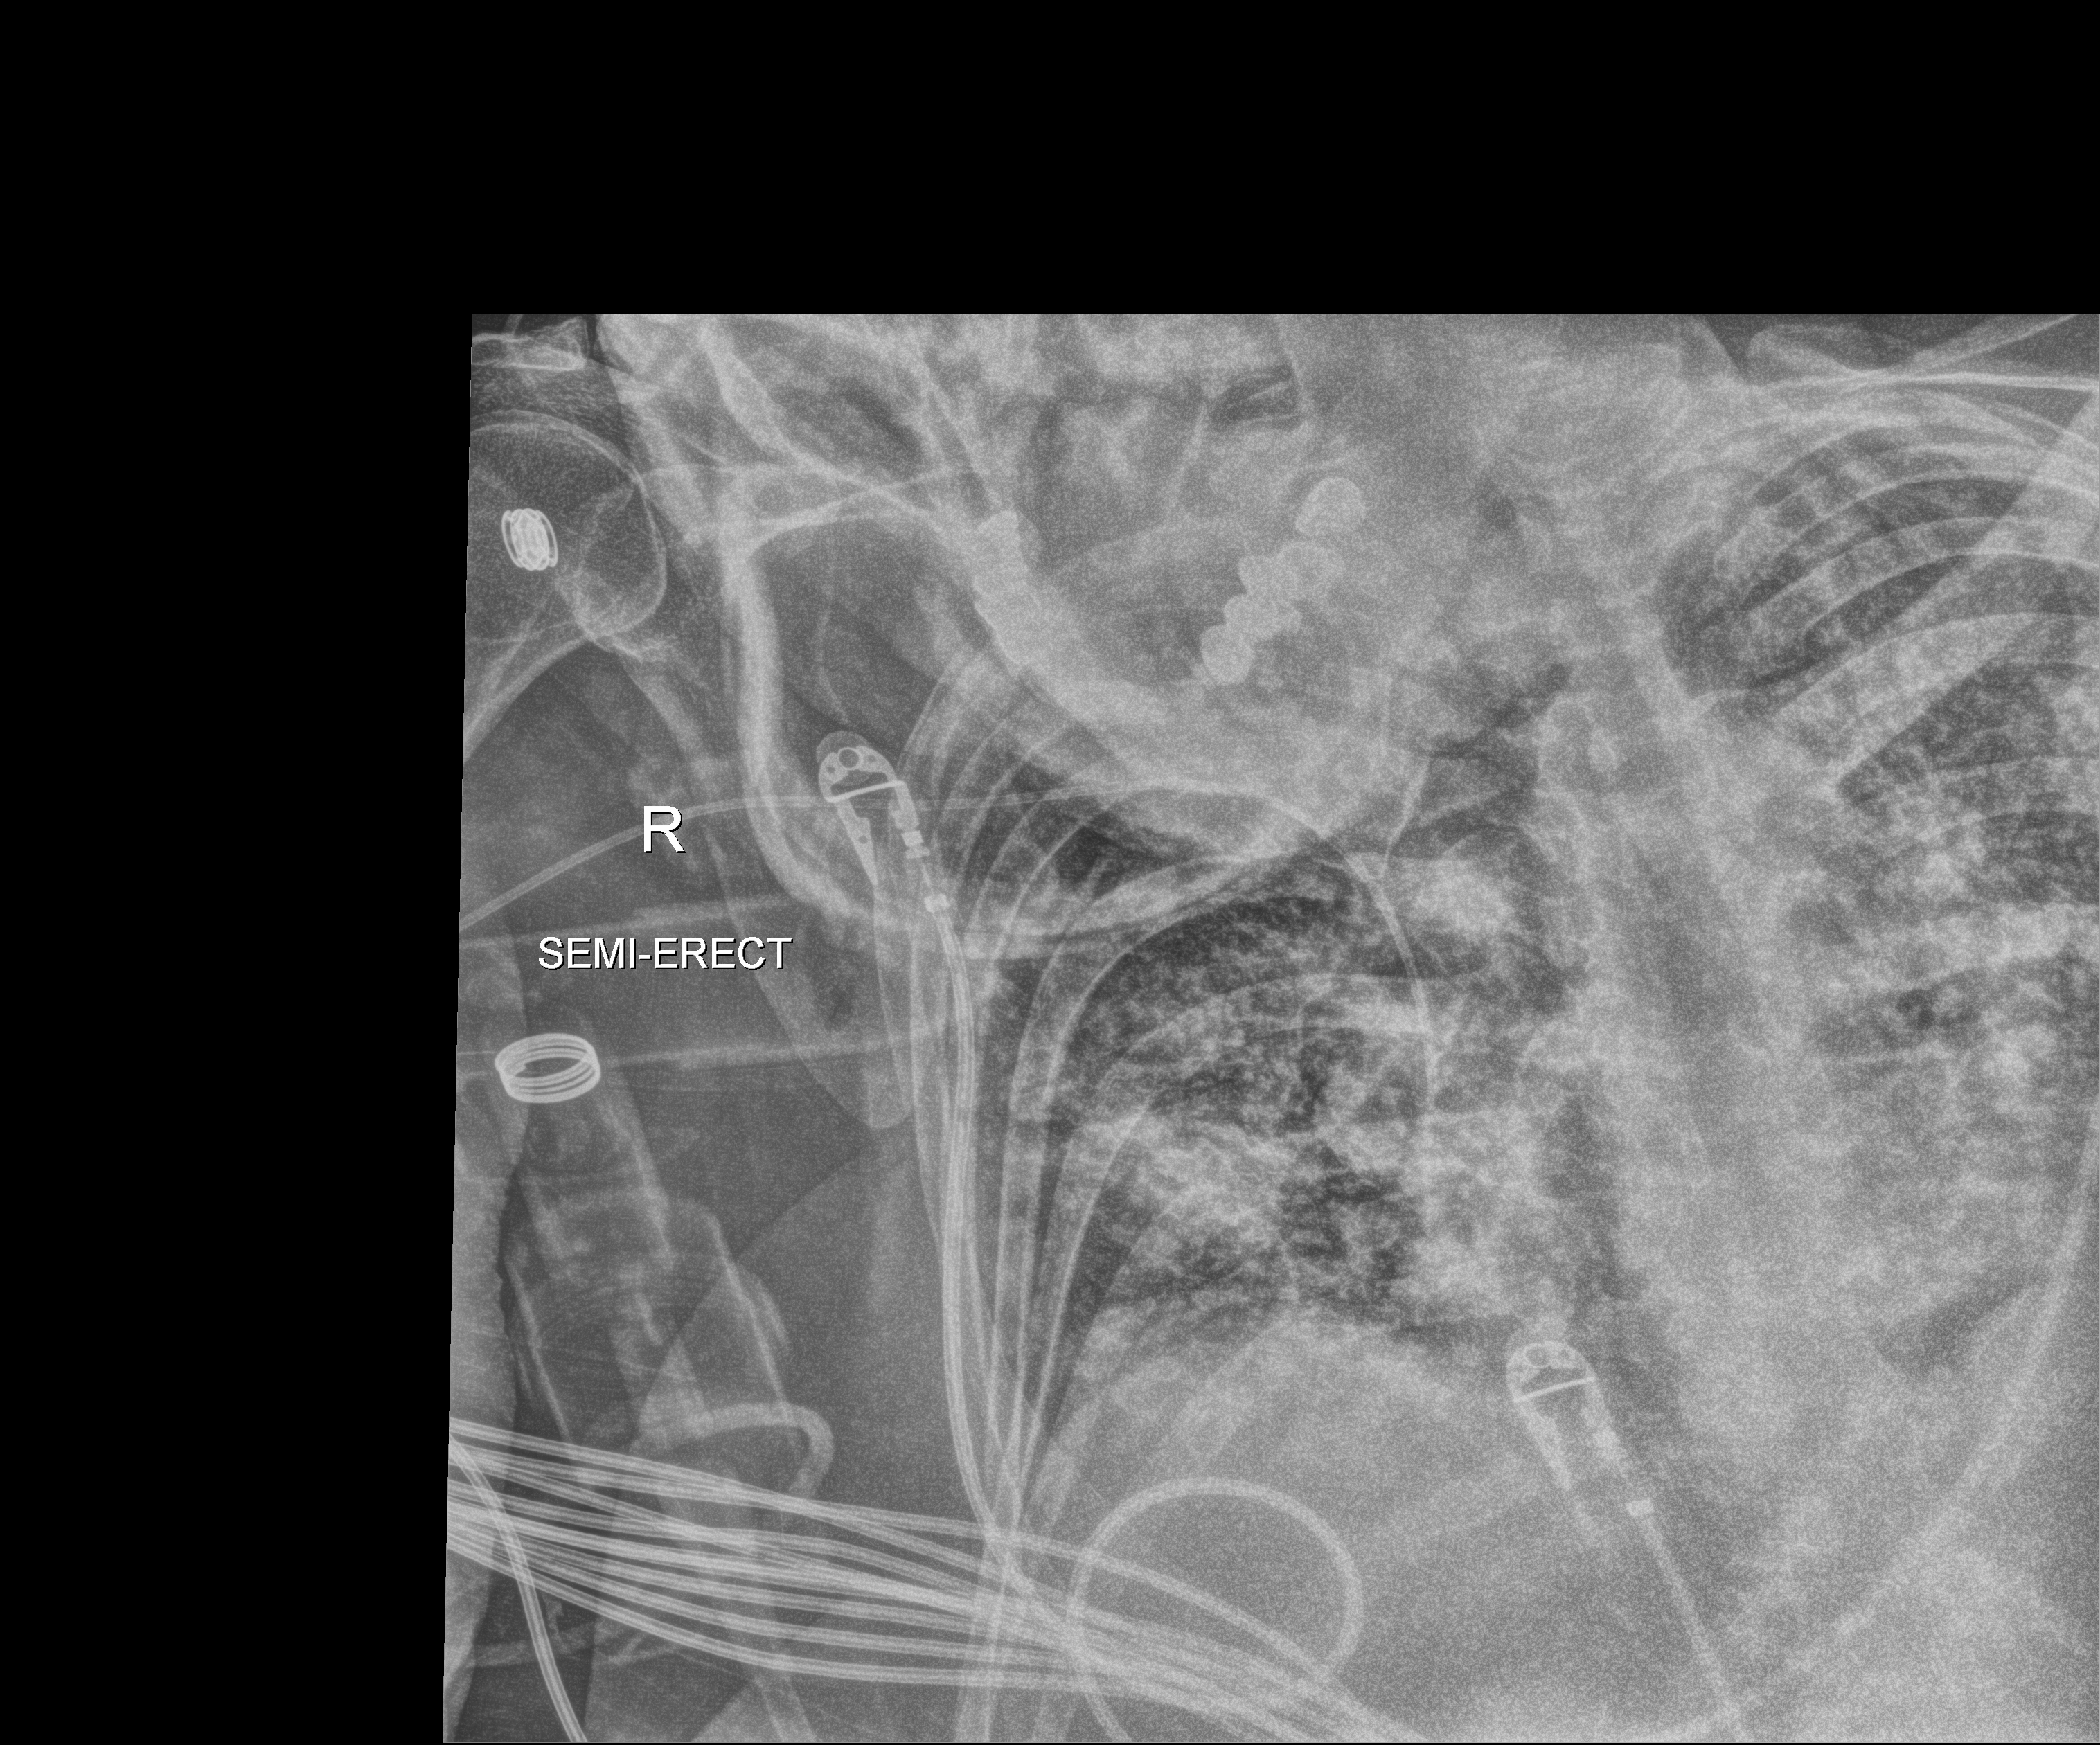
Portable chest radiograph, anteroposterior (AP) projection. Patient hospitalised with COVID-19; female, aged 60–74 years.
Admission-level facts for this patient (not findings on this image; timing relative to this image not recorded): COPD (admission record): no; mechanically ventilated during this hospital stay: yes; admitted to intensive care during this hospital stay: yes.